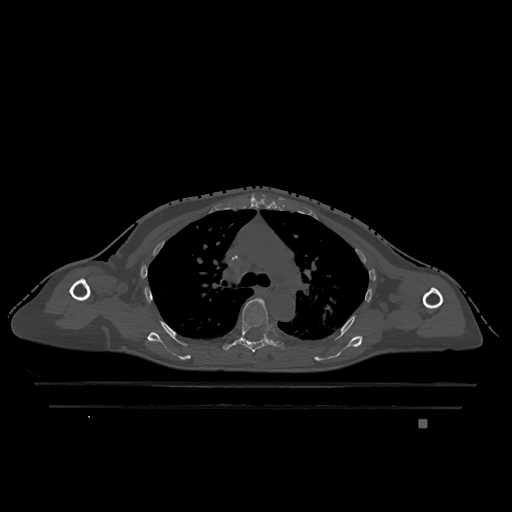
CT including the spine, one axial slice; position 839 of 1317 along the scan axis; bone window (W 1800 / L 400 HU); 512 × 512 image matrix. Female patient, age 74 years. From the clinical record (not read from this slice): primary cancer: lung.
Structures marked on this image (semi-automatically segmented with operator editing):
- T5 vertebra: bounding box <223,298,284,353> (left, top, right, bottom; pixels)